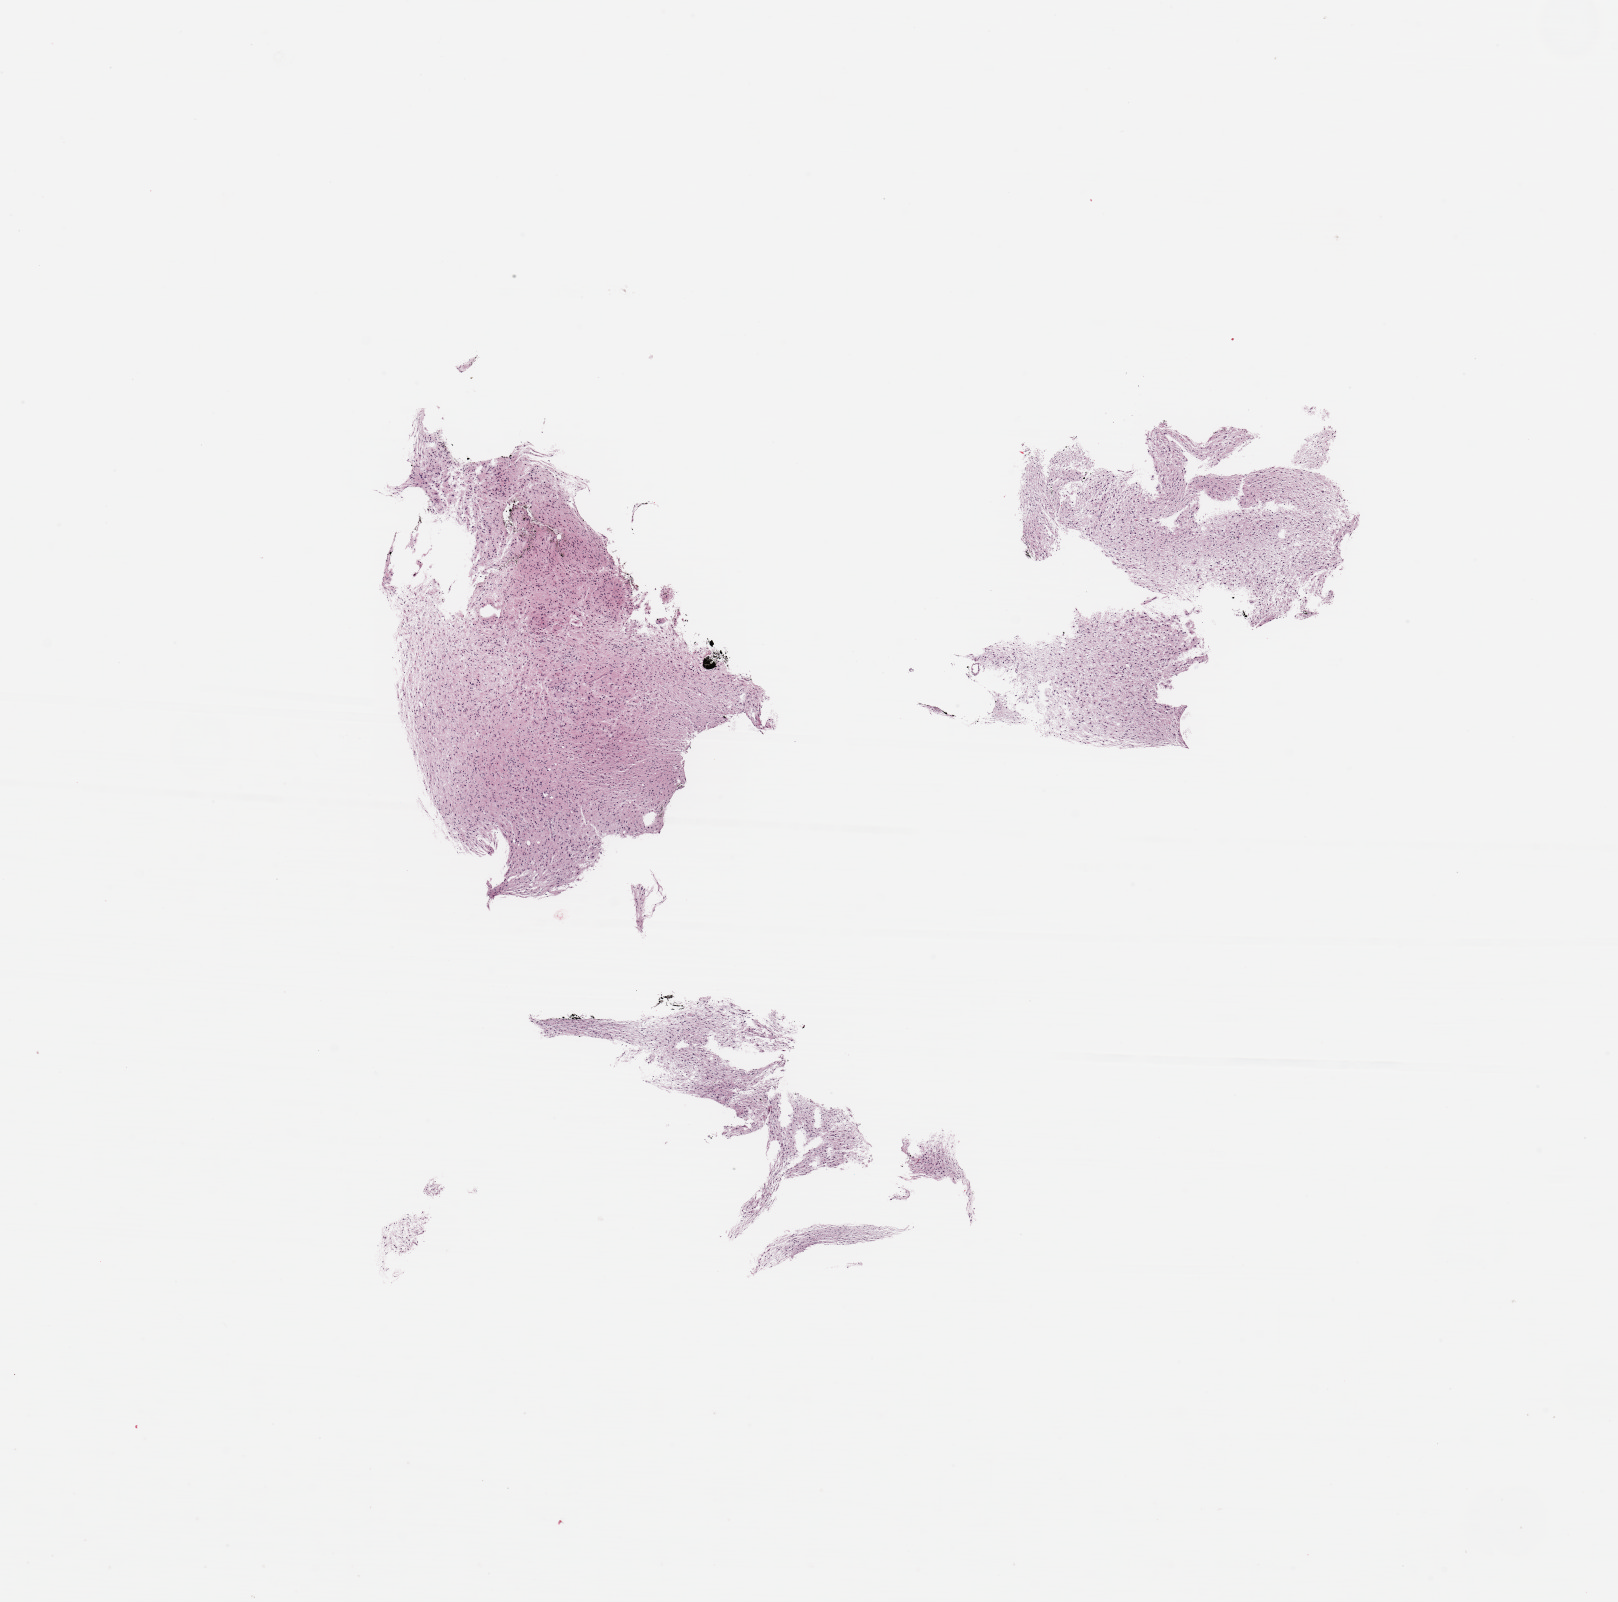
Digitized H&E tissue section (whole slide), a low-resolution overview of the entire scanned area, about 12.8 x 12.7 mm (slide scanned at 20x); tumour tissue sample, sampled site: frontal lobe. 34-year-old male patient. Composition of this section per pathologist review: tumour nuclei 80%, necrosis 3%.
• primary tumour site (as recorded): frontal lobe
• diagnosis: Glioblastoma